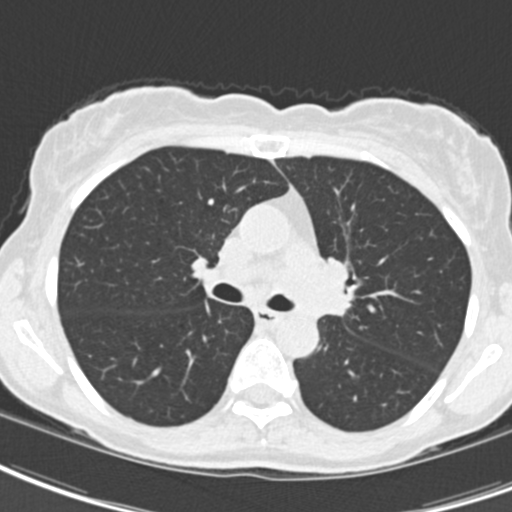
Low-dose screening chest CT, one axial slice; slice 125 of 189 in the series (ordered by position); reconstruction kernel B30f; 120 kVp; lung window (W 1500 / L -600 HU); 512 × 512 image matrix, field of view 279 × 279 mm.
Annotated regions visible in this slice (outlined manually by an expert reader):
- lesion 2 (tumor, hilum of left lung): bounding box (x1, y1, x2, y2) in pixels: (283, 258, 351, 314)